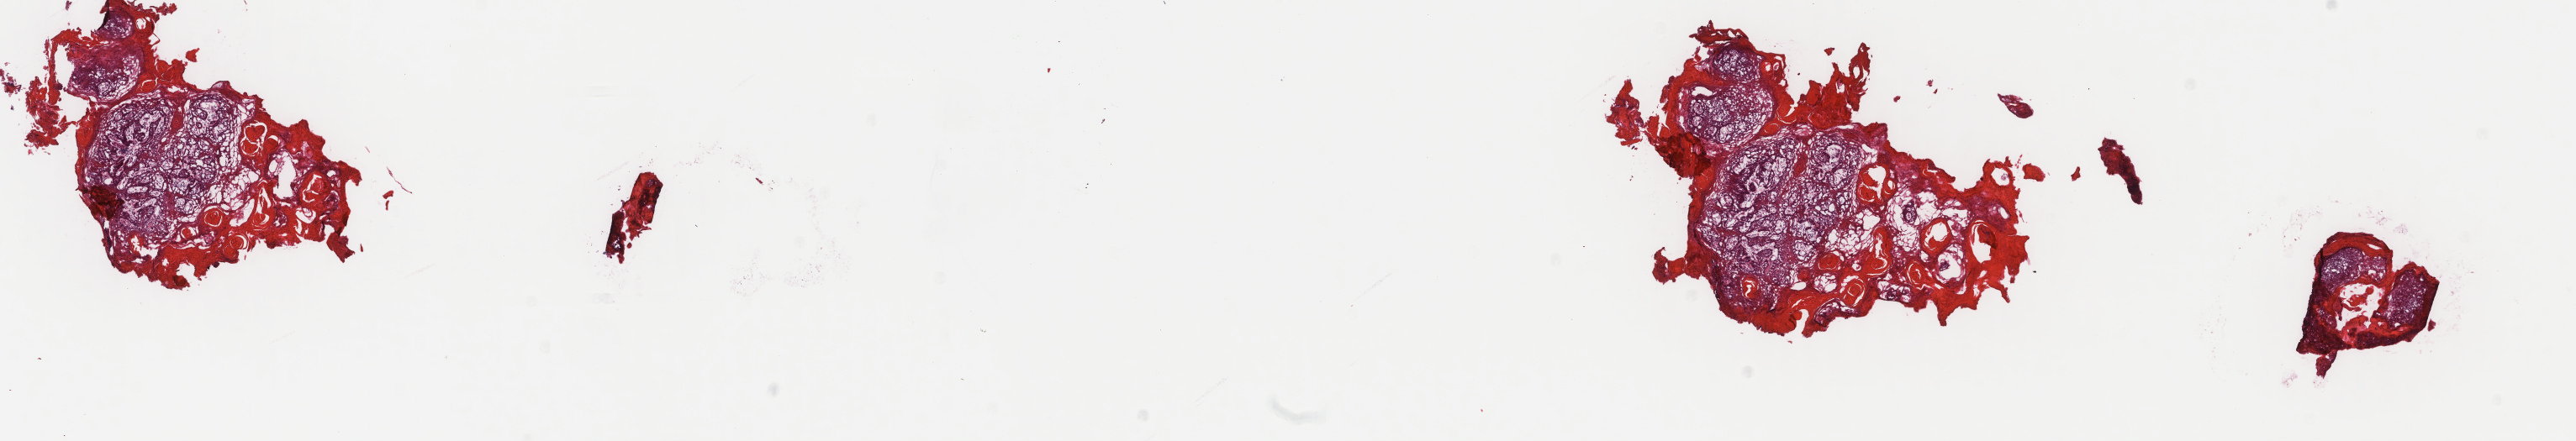
Whole-slide histology image, H&E-stained — a low-resolution overview of the entire scanned area, about 24.3 x 4.2 mm, frozen section from the top of the tissue portion, head and neck, primary tumour sample. Female patient; age at initial diagnosis 85 years. Composition of this section per pathologist review: tumour cells 80%, tumour nuclei 80%.
Histologic diagnosis: Squamous cell carcinoma, NOS (tongue, NOS).